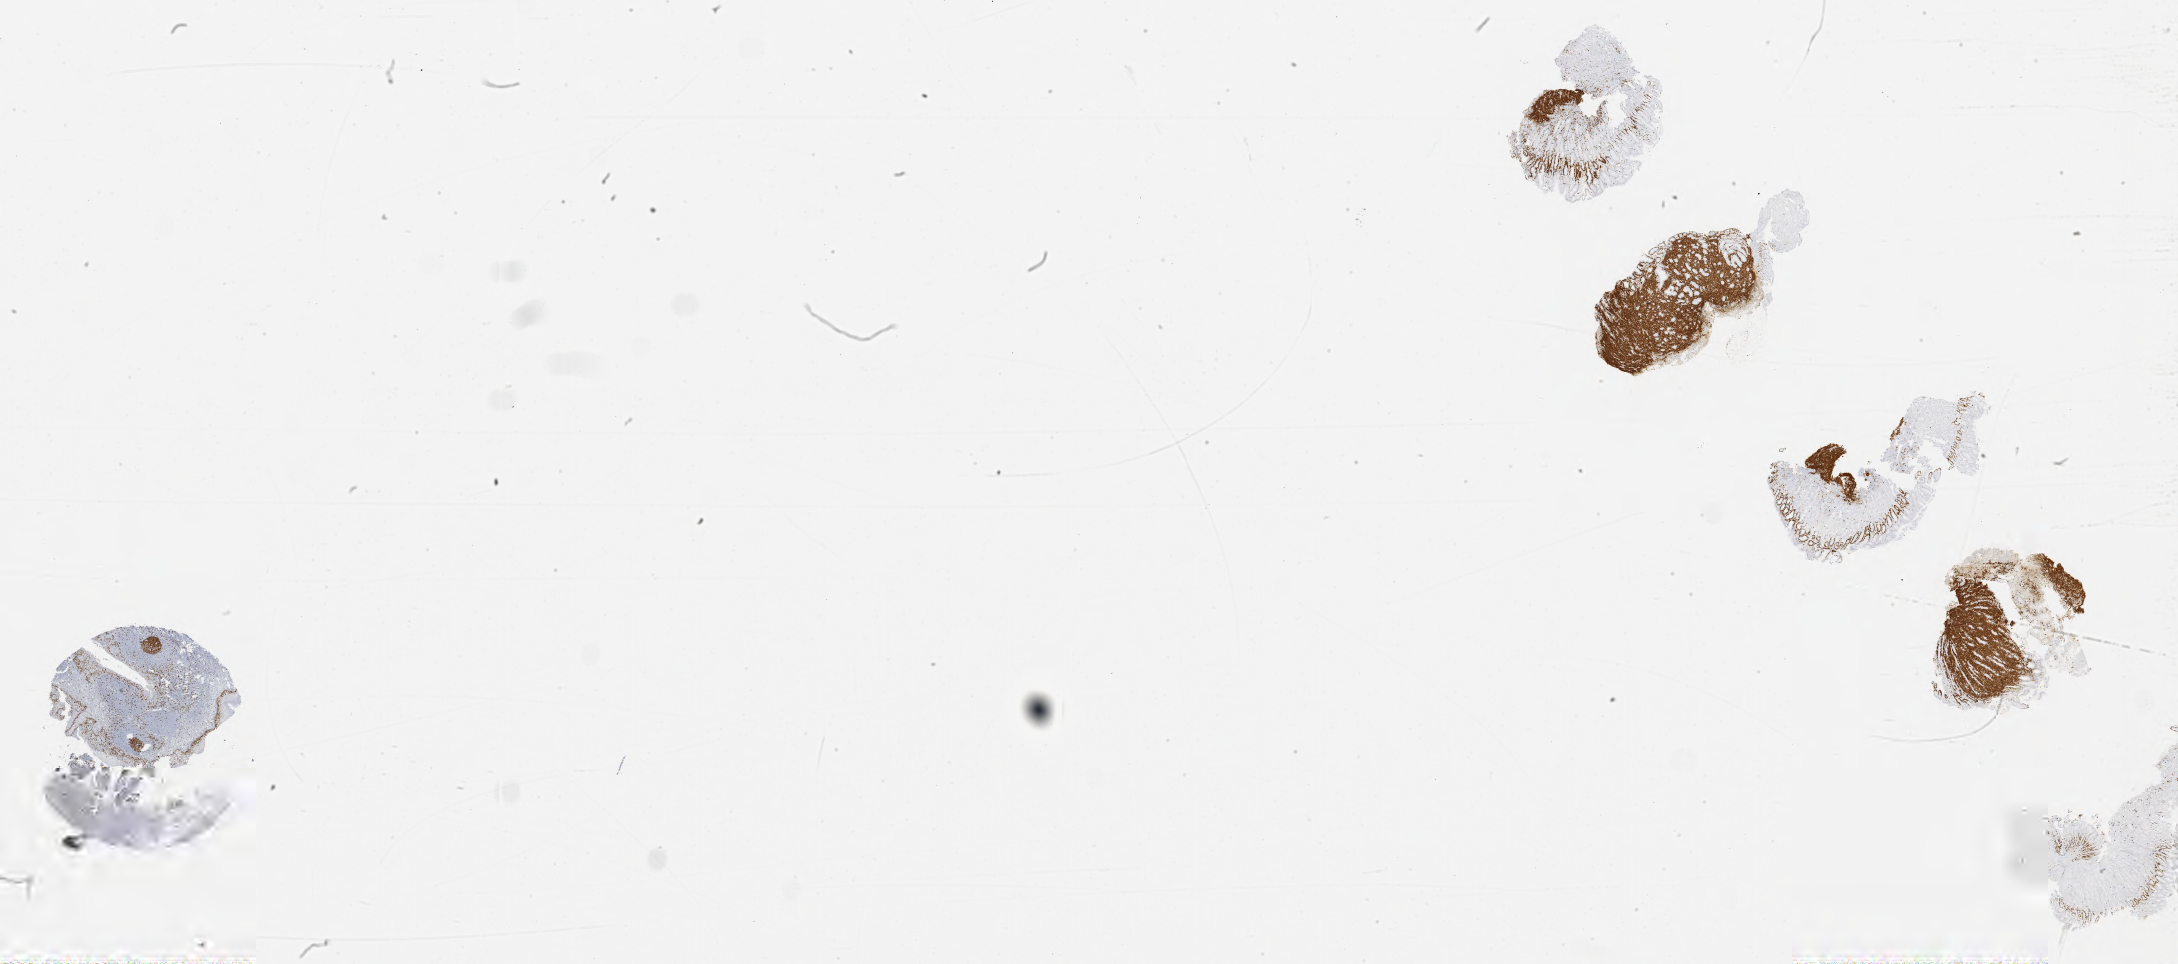
IHC for Ki-67, whole-slide image, shown as a low-resolution overview of the whole scanned area (about 35.0 x 15.5 mm), specimen: tumor tissue. Male patient, age 40 years.
- histologic diagnosis: Burkitt lymphoma, NOS